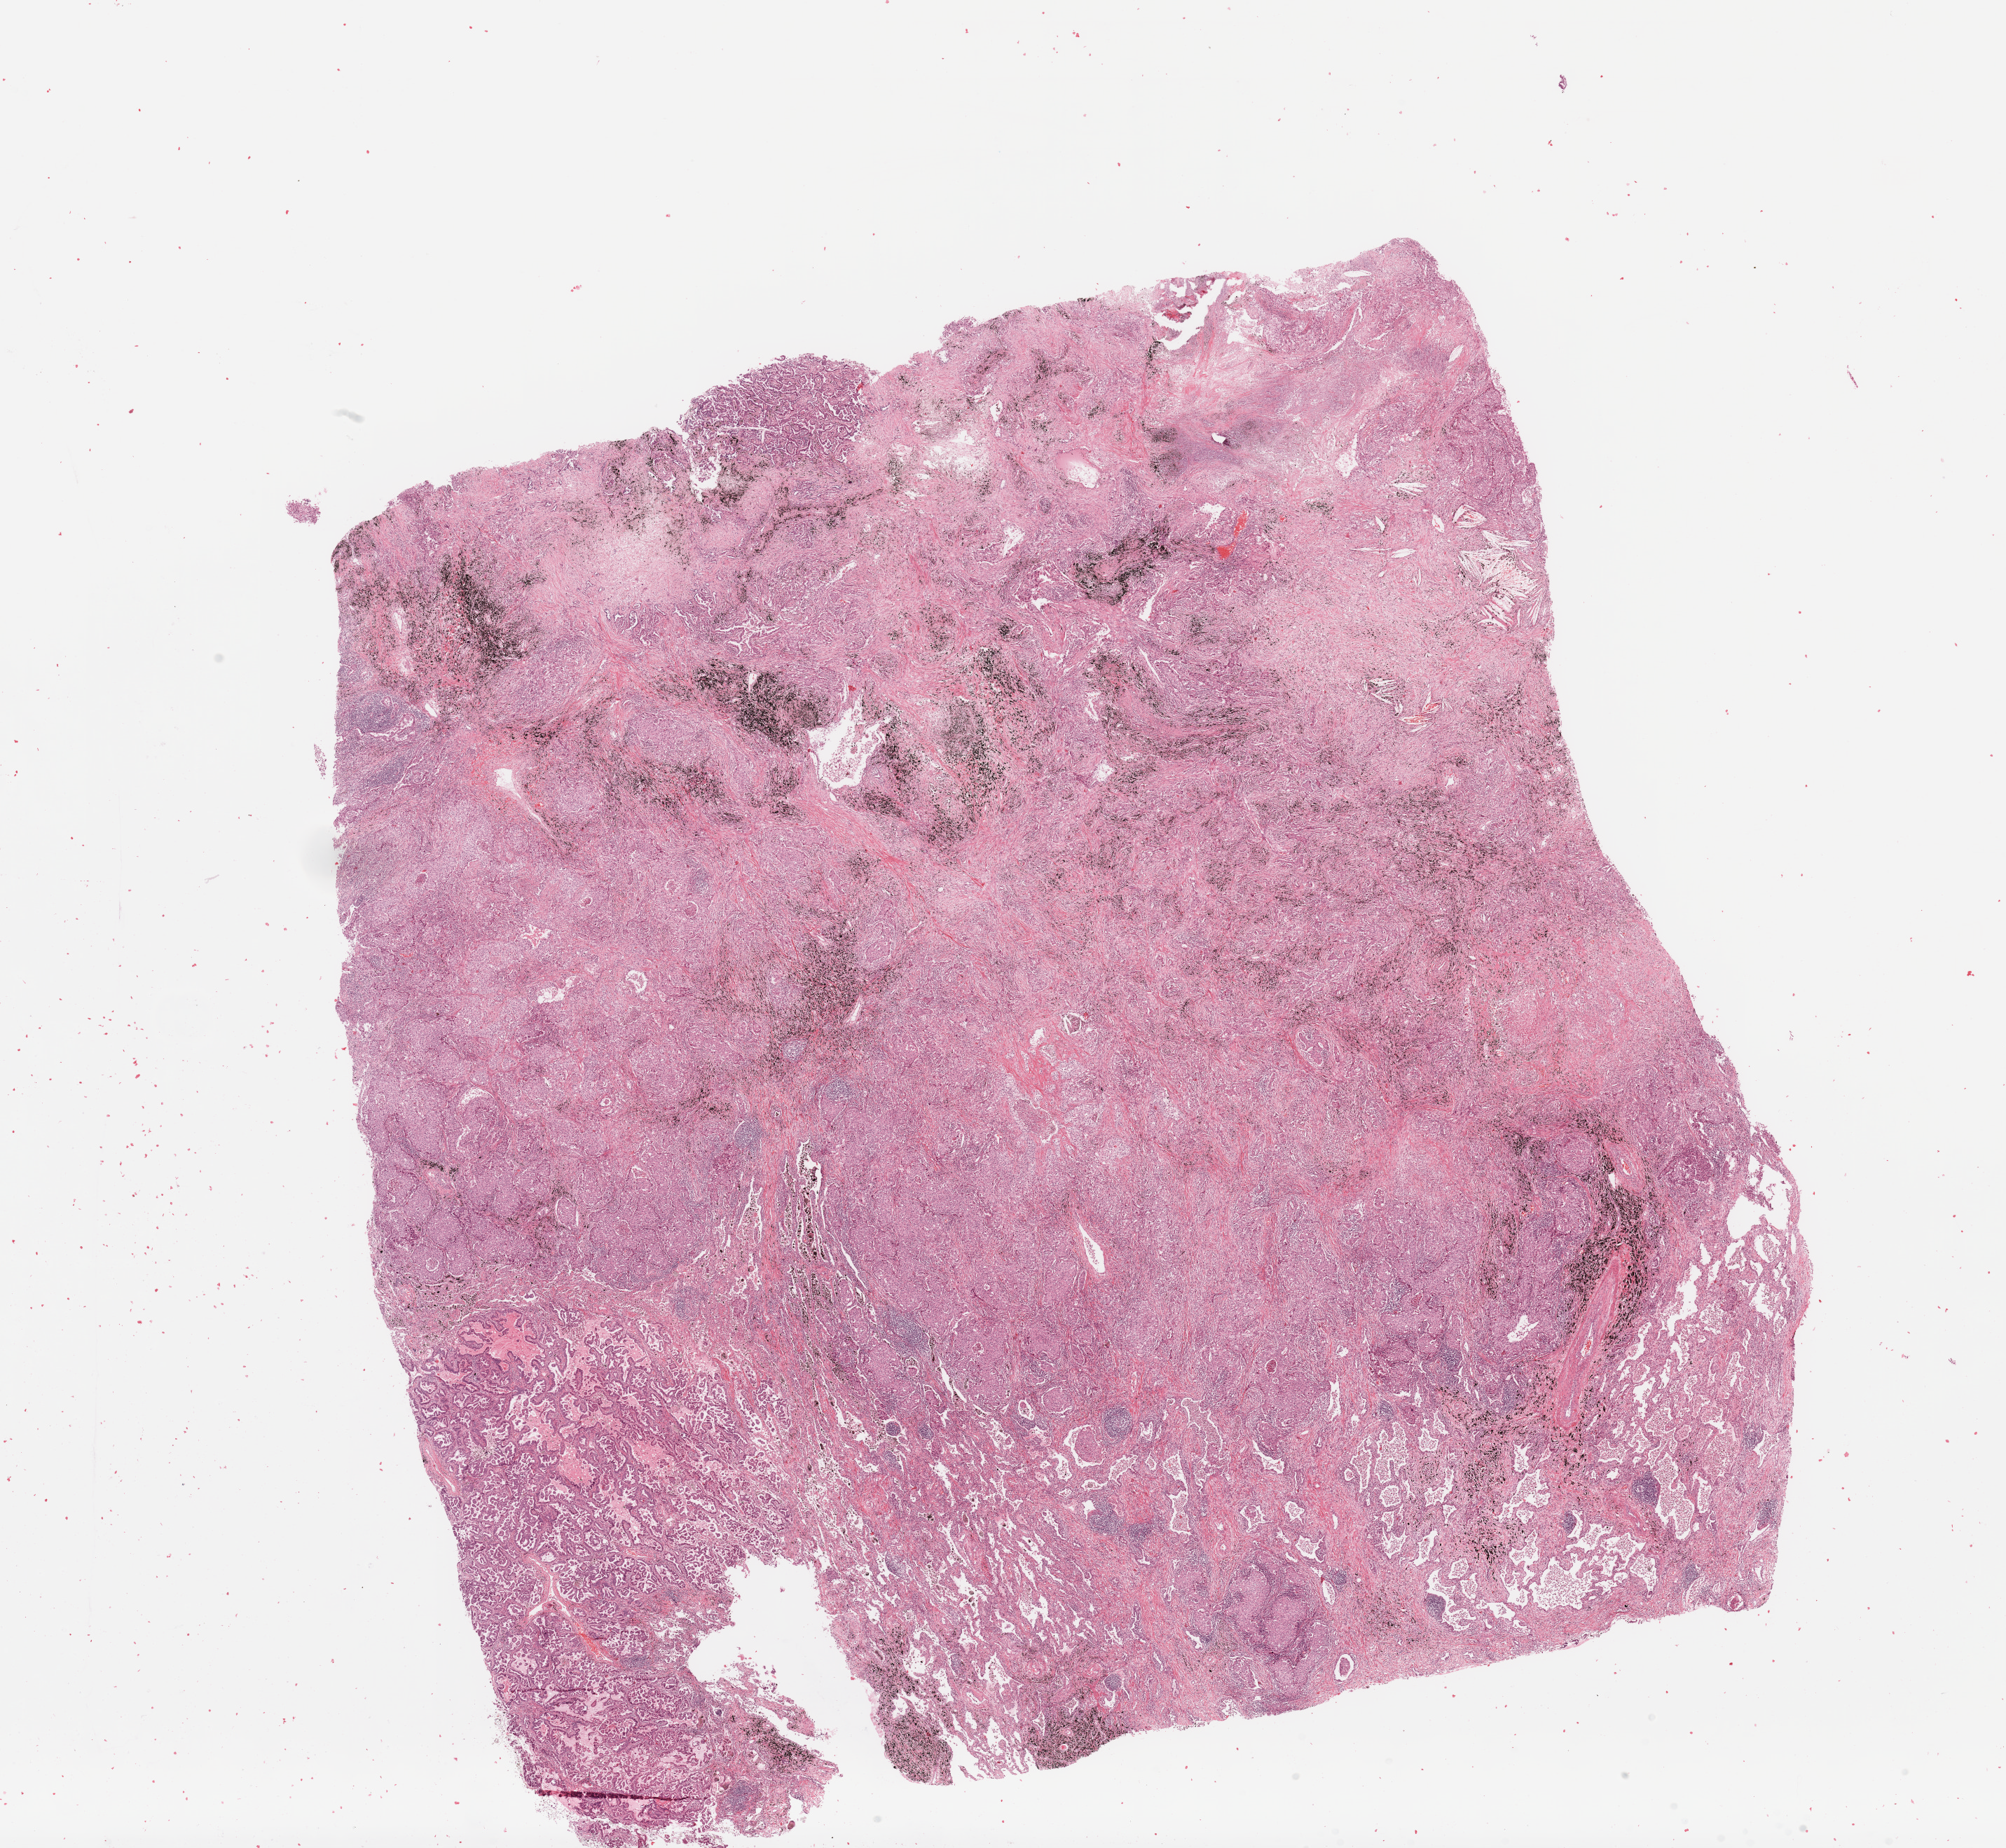
Whole-slide histology image, Hematoxylin and eosin (H&E) stained, whole scanned area (about 22.6 x 20.9 mm) shown as a low-resolution overview. Tumour tissue sample, lung. Male, 58 y/o. Histologic grade: G3 (poorly differentiated).
AJCC pathologic stage: IIA. Histologic diagnosis: Adenocarcinoma, NOS.